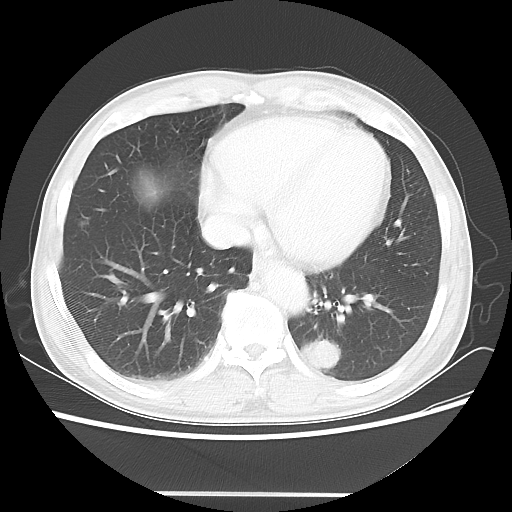
Chest CT, one axial slice; position 18 of 60 along the scan axis; reconstruction kernel LUNG; 100 kVp; lung window (W 1500 / L -600 HU); 5 mm slice thickness; 512 × 512 image matrix, field of view 360 × 360 mm. Male patient, age 55 years. Case-level facts recorded for this patient, not image findings: clinical TNM (as recorded): T1c N3 M0; histopathological grade: G3.
Annotated regions visible in this slice (bounding box drawn by a radiologist):
- lung tumour (recorded histology: small cell carcinoma): box from (x=296, y=337) to (x=347, y=376) px